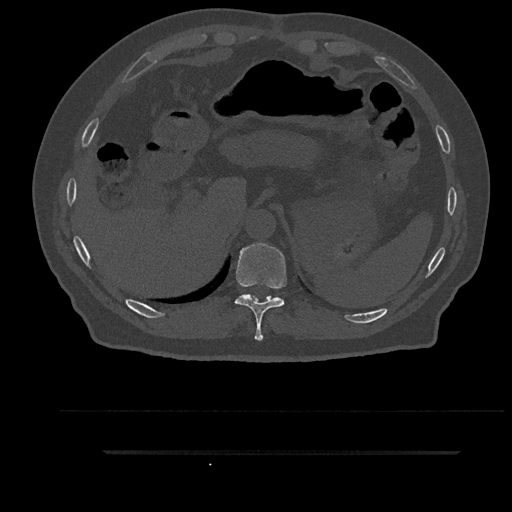
CT including the spine, one axial slice. Position 355 of 797 along the scan axis. Reconstruction kernel Br40s/3. 120 kVp. Bone window (W 1800 / L 400 HU). 0.5 mm slice thickness. 512 × 512 image matrix, field of view 432 × 432 mm. Male patient, age 63 years. From the clinical record (not read from this slice): primary cancer: renal.
Outlined on this slice (semi-automatic segmentation, software-assisted and operator-edited):
- T10 vertebra: bounding box [x1, y1, x2, y2] px = [235, 243, 287, 341]
- T11 vertebra: [244, 294, 278, 298]